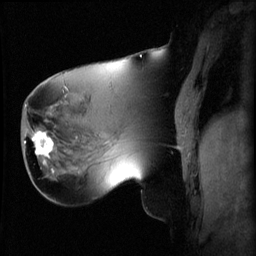
Breast MRI (dynamic contrast-enhanced), one sagittal slice. Slice 23 of 60 in the series (ordered by position). 3 images stored at this slice position (order not interpretable as contrast timing). 1.5 T. TE 4.2 ms, TR 8.2 ms. 256 × 256 image matrix, field of view 220 × 220 mm. Female patient, age 62 years.
Annotated regions visible in this slice (semi-automatic segmentation, software-assisted and operator-edited):
- analysis volume of interest (the breast-tissue region the enhancement analysis was run in; not a lesion): bounding box <26,126,59,165> (left, top, right, bottom; pixels)
- tumour enhancement mask (voxels above the 70 % enhancement threshold inside the analysis volume of interest): <32,132,55,159>